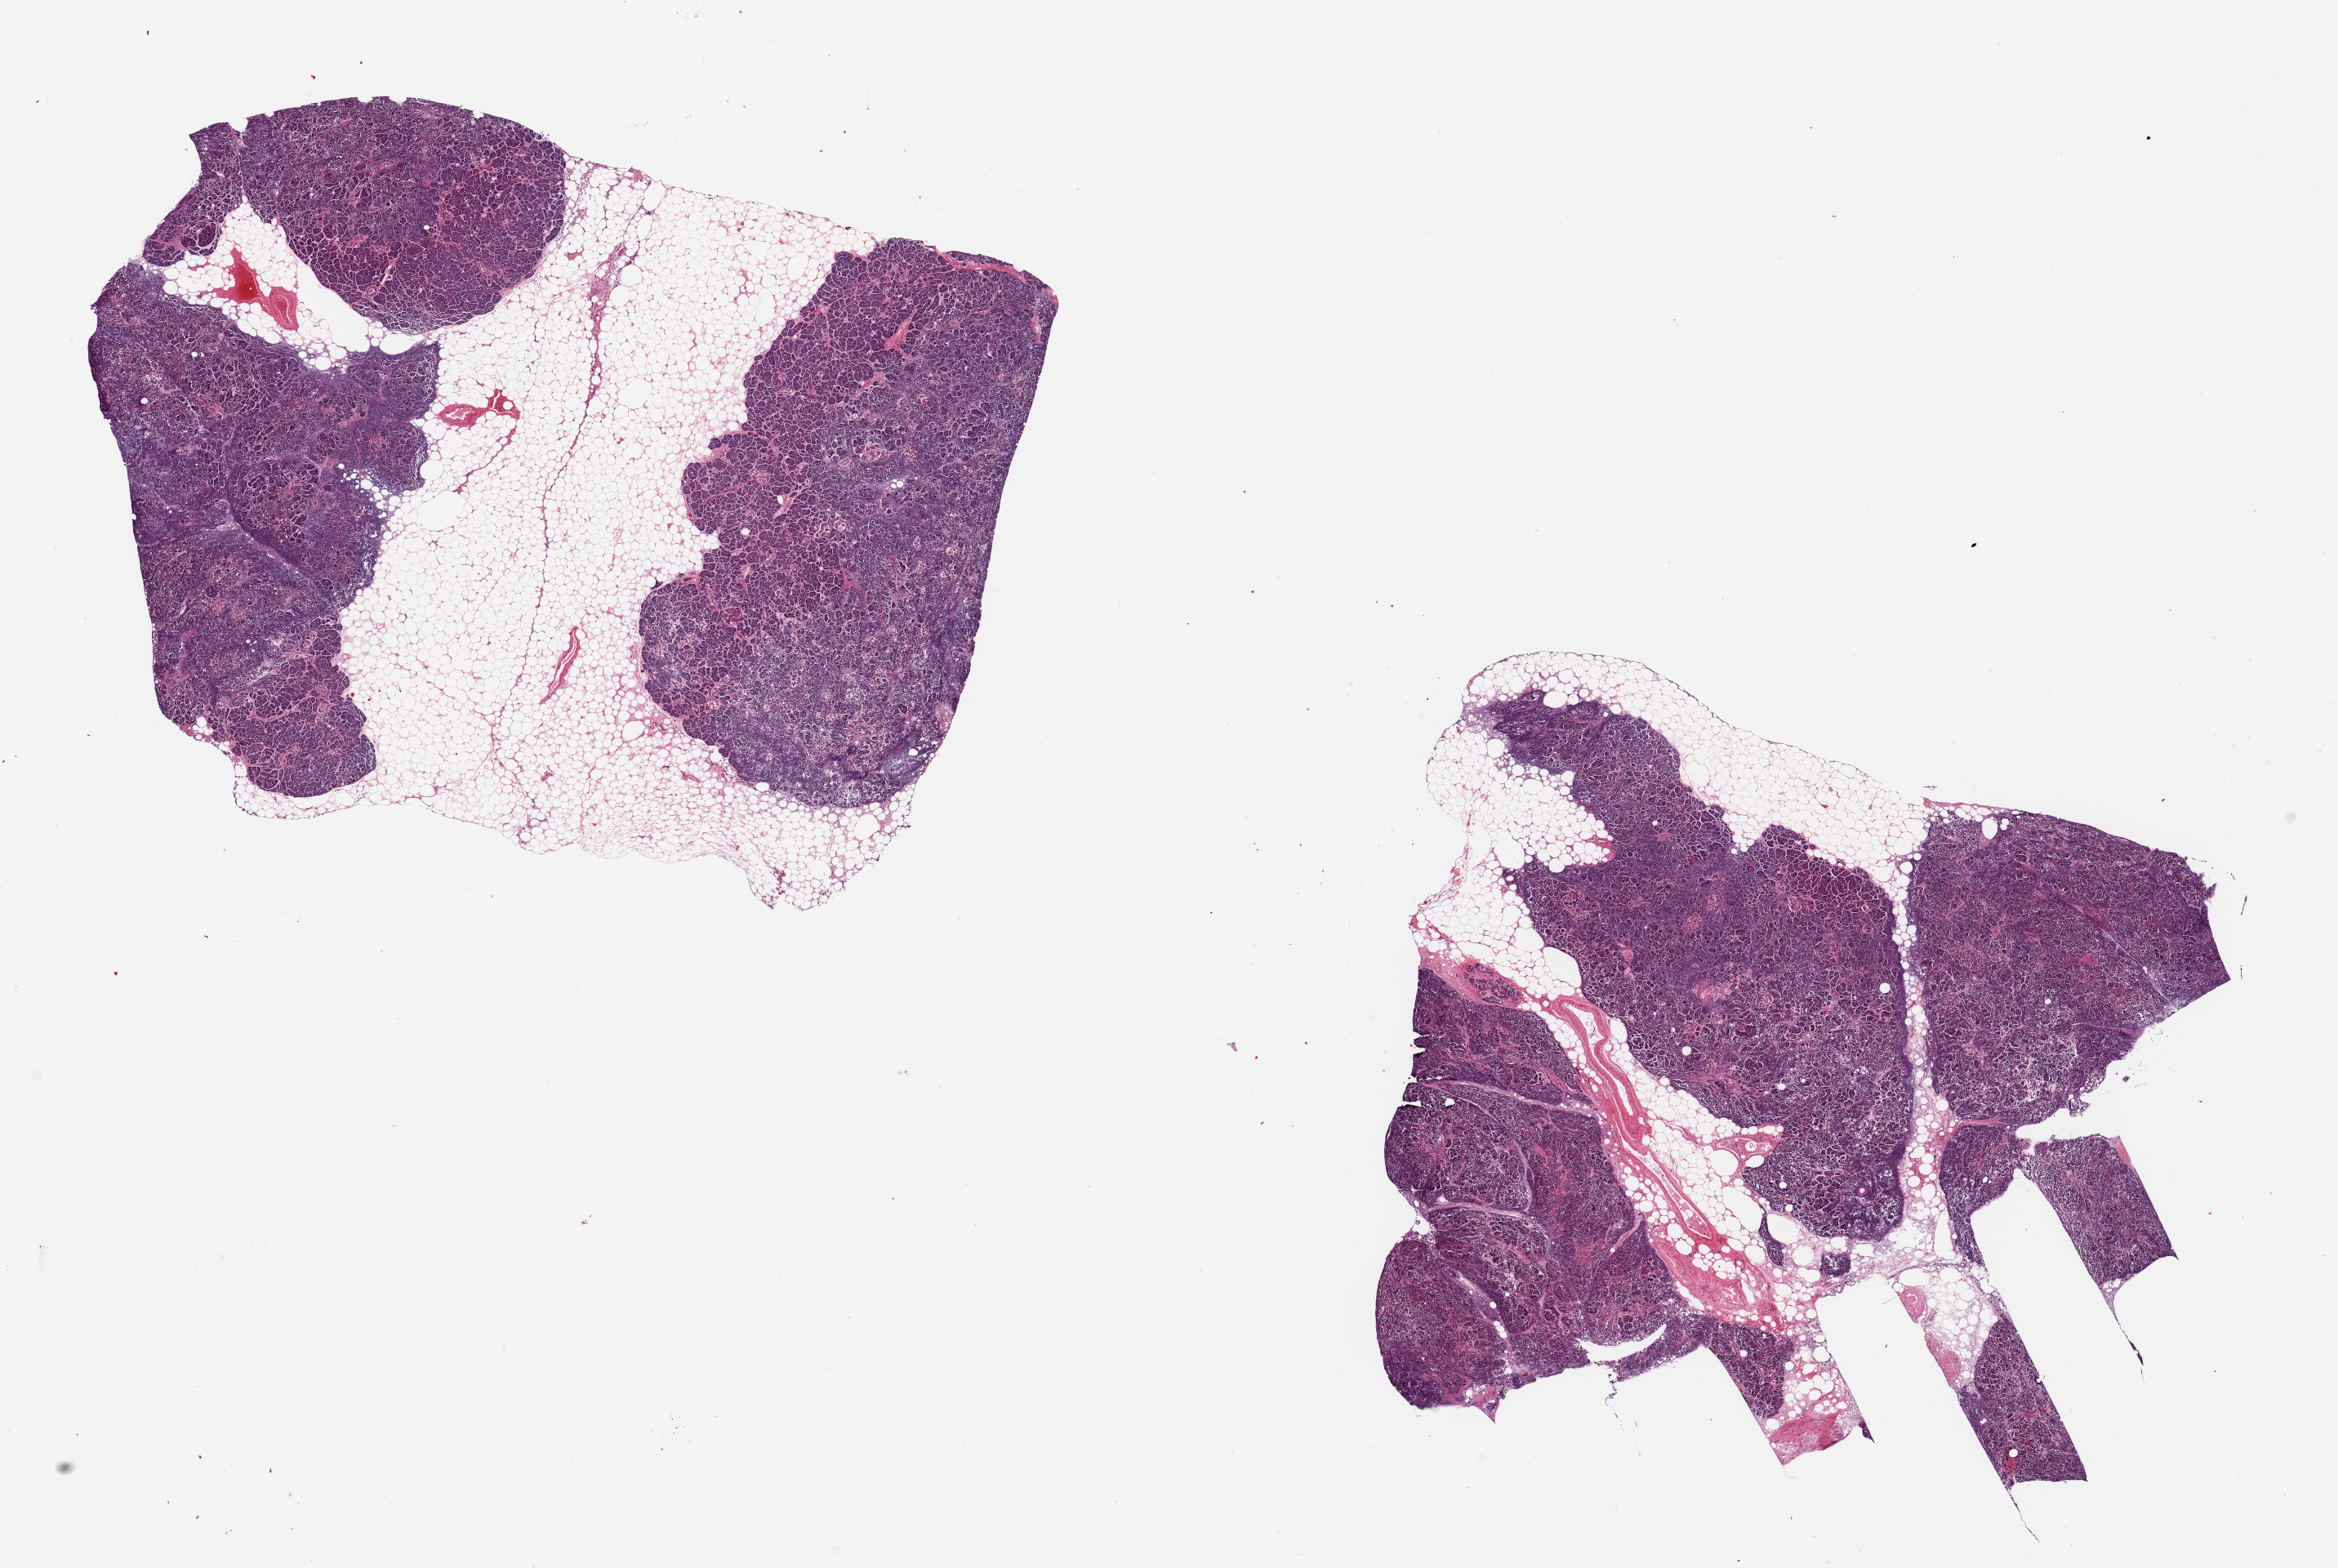
Whole-slide image, hematoxylin and eosin (H&E) stain, brightfield — whole scanned area (about 22.6 x 15.2 mm) shown as a low-resolution overview, PAXgene-fixed, paraffin-embedded tissue, target tissue: pancreas, donor tissue sample.
Reviewer comment on this tissue sample: 2 pieces, 9x7 & 10x9.5mm; embedded adipose 20-40 %.